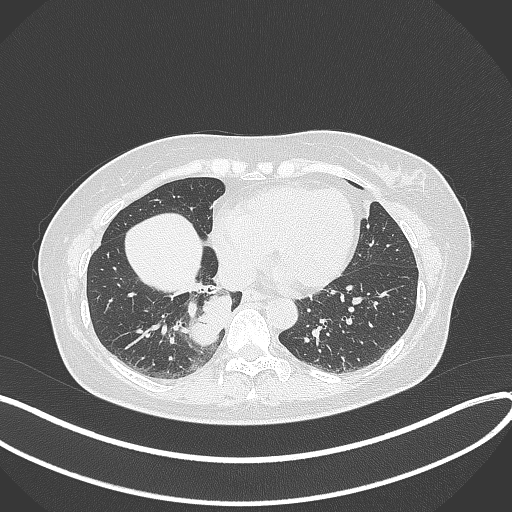
Chest CT, one axial slice; slice 114 of 331 in the series (ordered by position); 120 kVp; lung window (W 1500 / L -600 HU); 1 mm slice thickness; 512 × 512 image matrix, field of view 400 × 400 mm. Patient: female, 54 years. Case-level facts recorded for this patient, not image findings: clinical TNM (as recorded): T4 N0 M0.
Outlined on this slice (bounding box drawn by a radiologist):
- lung tumour (recorded histology: adenocarcinoma): box from (x=188, y=289) to (x=230, y=347) px